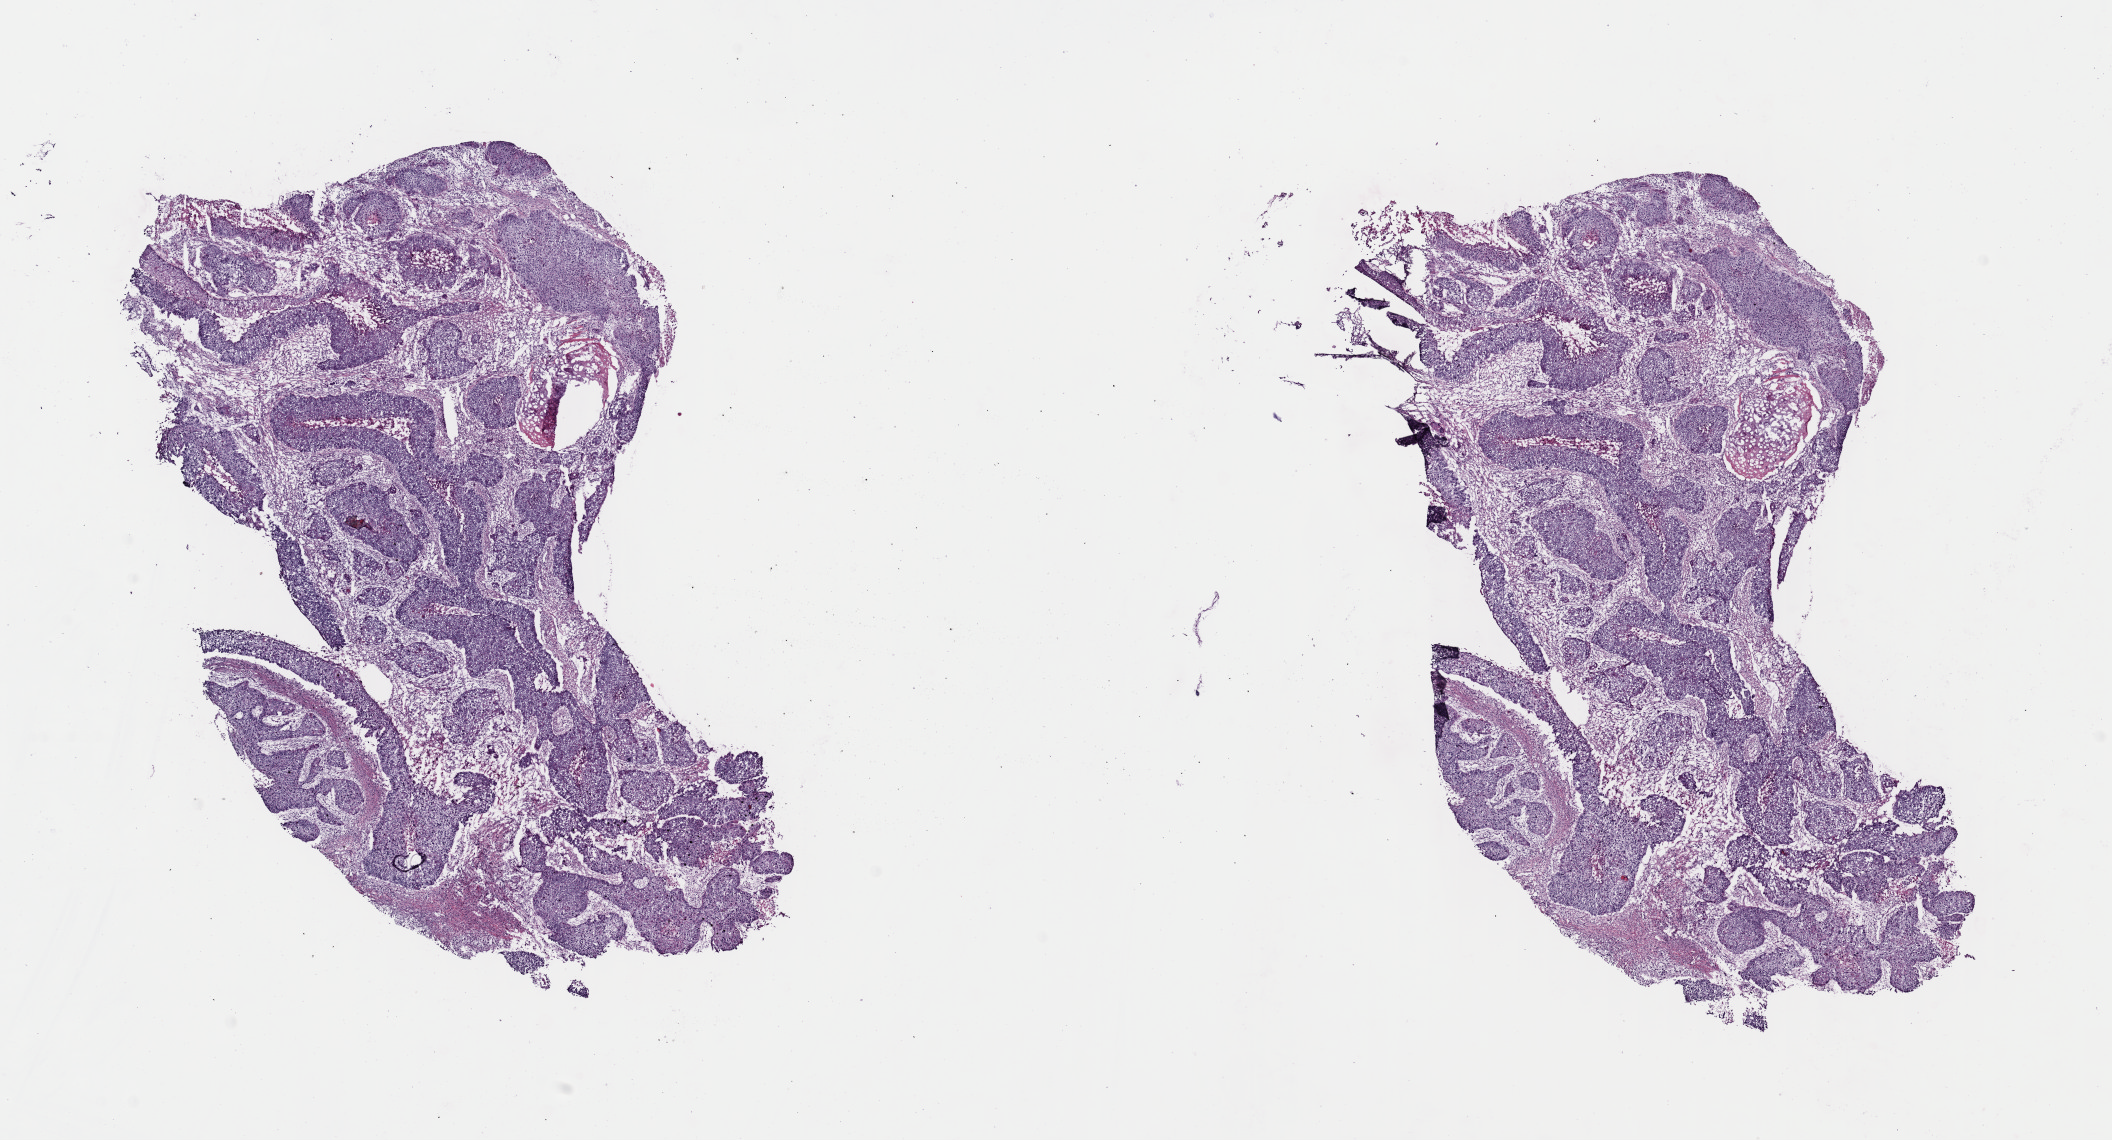
Whole-slide histology image, Hematoxylin and eosin (H&E) stained — a low-resolution overview of the entire scanned area, about 16.7 x 9.0 mm (acquisition: 40x scan), frozen section from the top of the tissue portion, lung, primary tumour sample. Patient: male, age at initial diagnosis 66 years. Slide review estimates, as recorded: tumour cells 95%, tumour nuclei 70%, normal cells 0%, stromal cells 0%, necrosis 5%. Inflammatory infiltration, as recorded: lymphocyte infiltration 0%, monocyte infiltration 0%, neutrophil infiltration 0%.
Histologic diagnosis: Squamous cell carcinoma, NOS (upper lobe, lung). AJCC pathologic stage: IIA (7th edition).